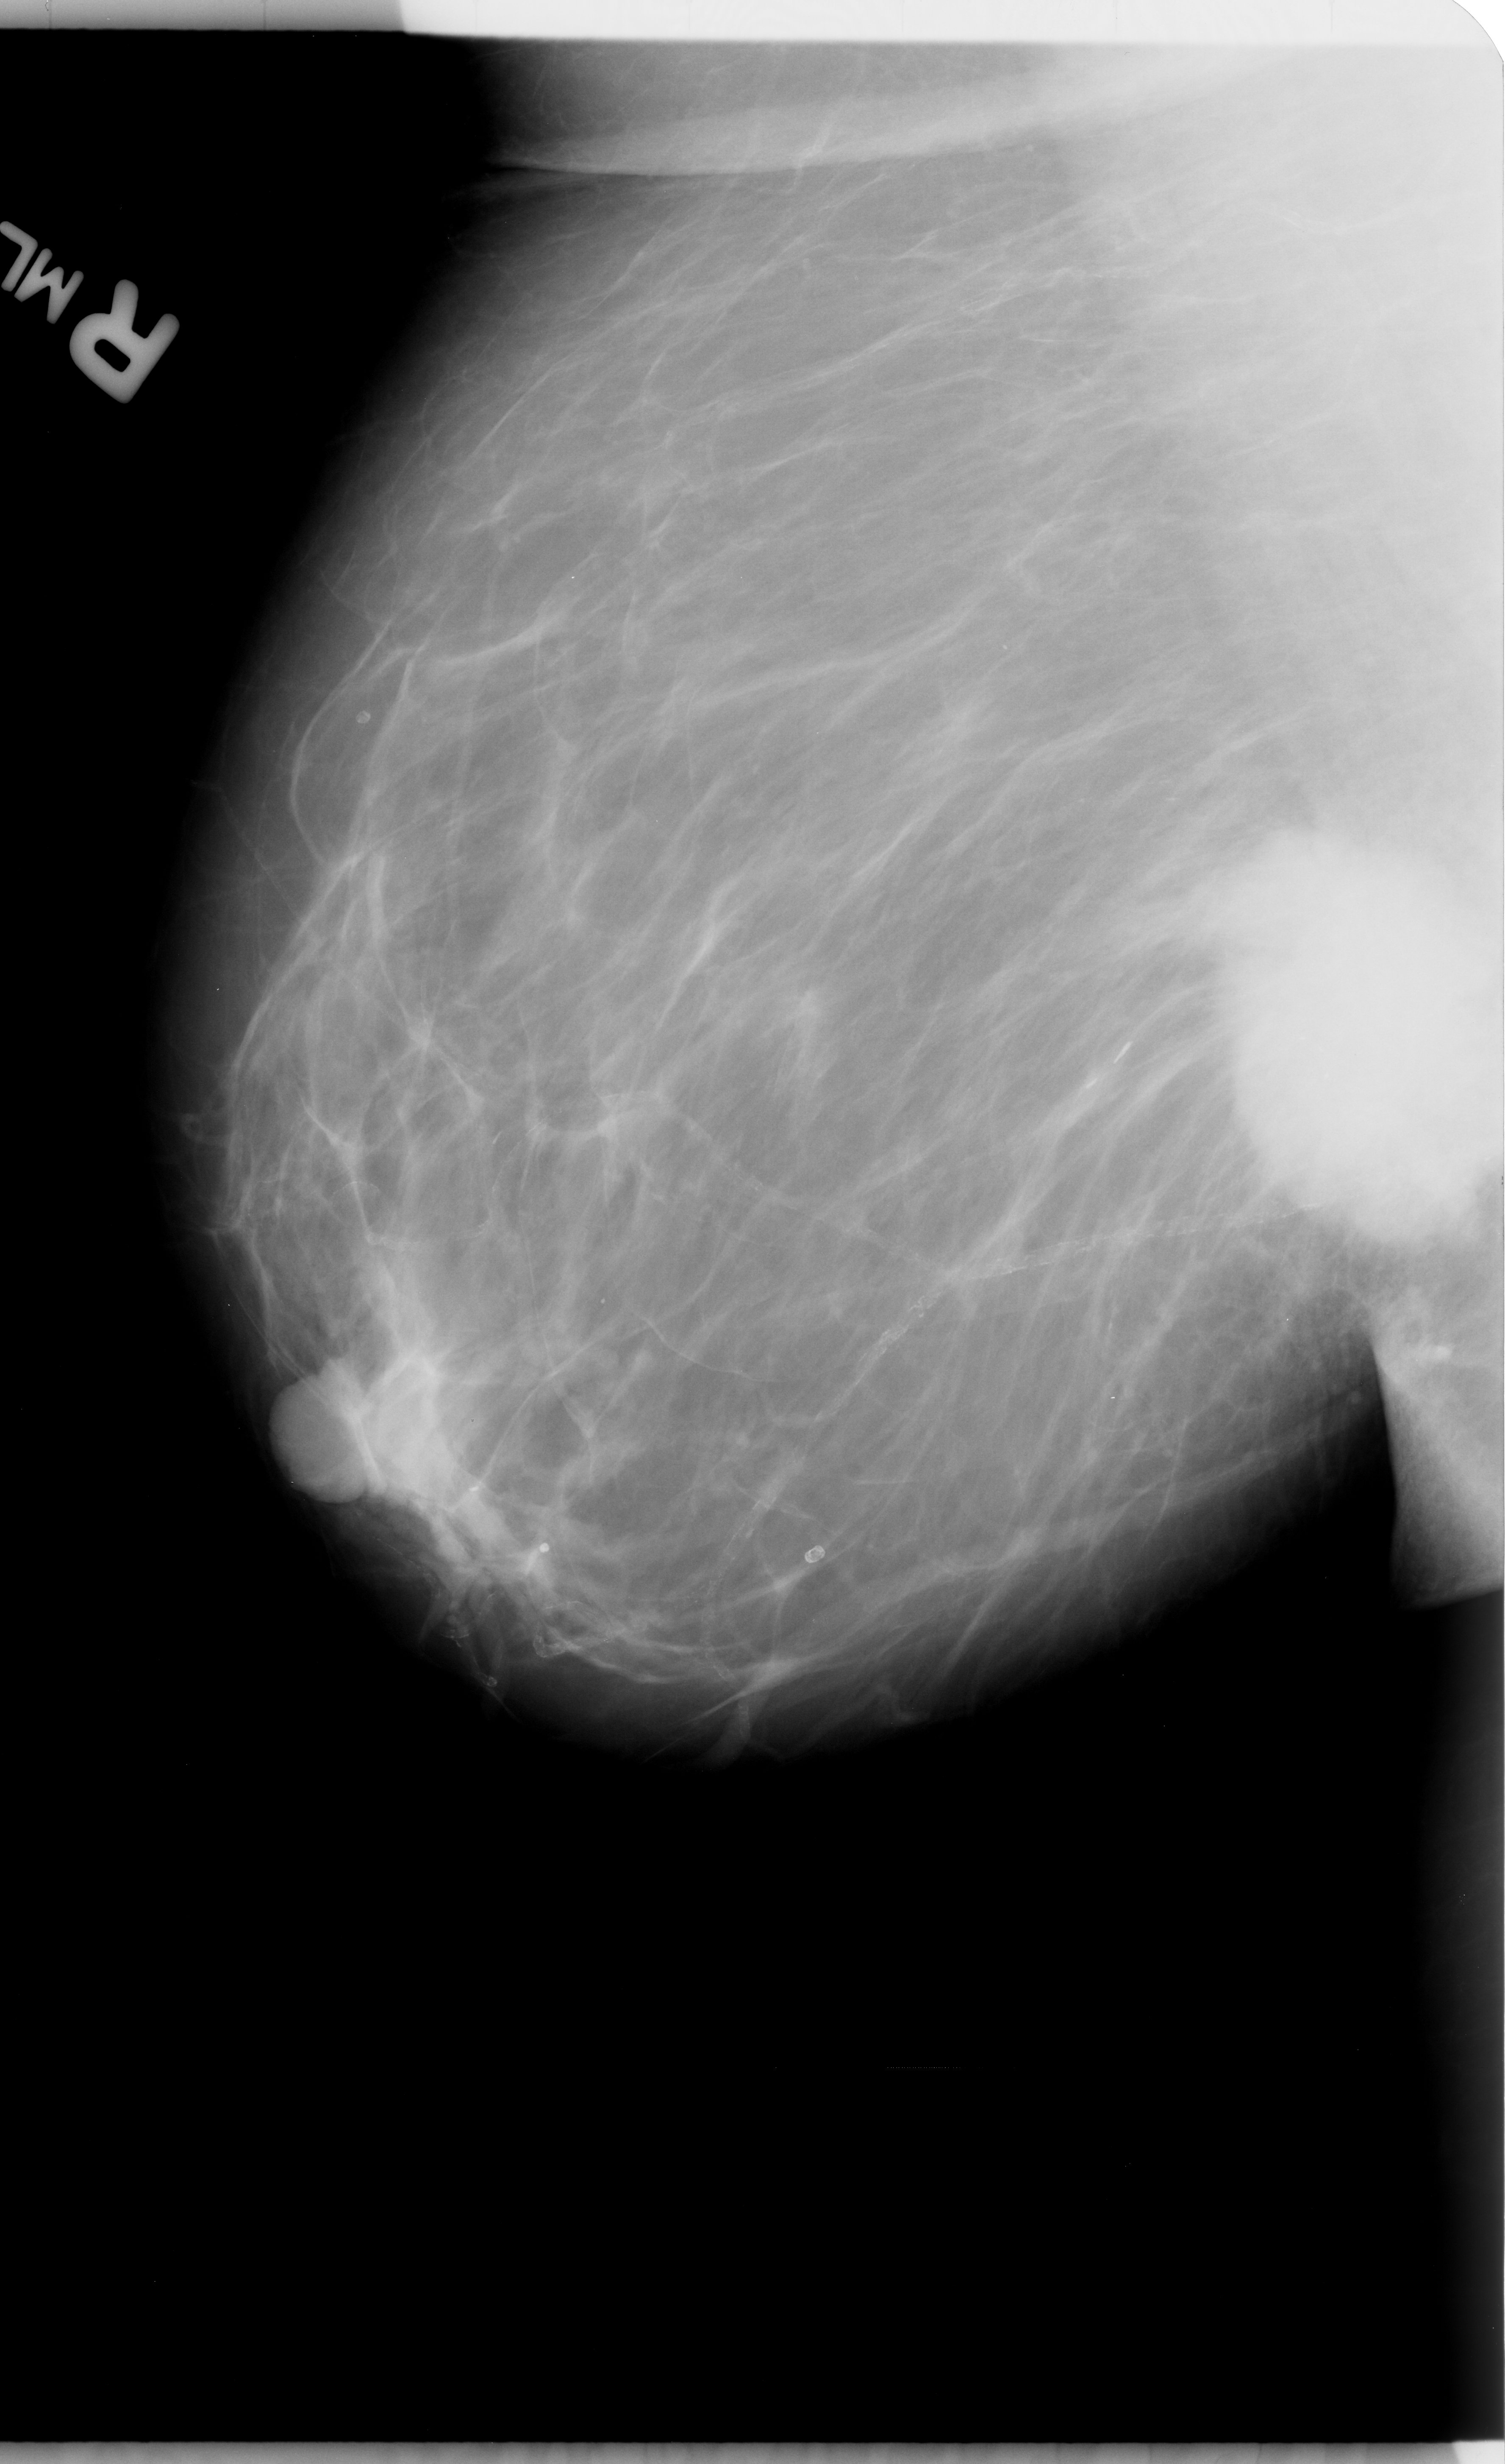
Mammogram (digitized film); right breast; MLO view; 1505 × 2464 image matrix.
Marked abnormalities (boxes around the expert regions of interest):
- mass, shape irregular, margins spiculated; BI-RADS assessment category 4; pathology result (as recorded, not read from the image): malignant: box from (x=1226, y=878) to (x=1505, y=1216) px